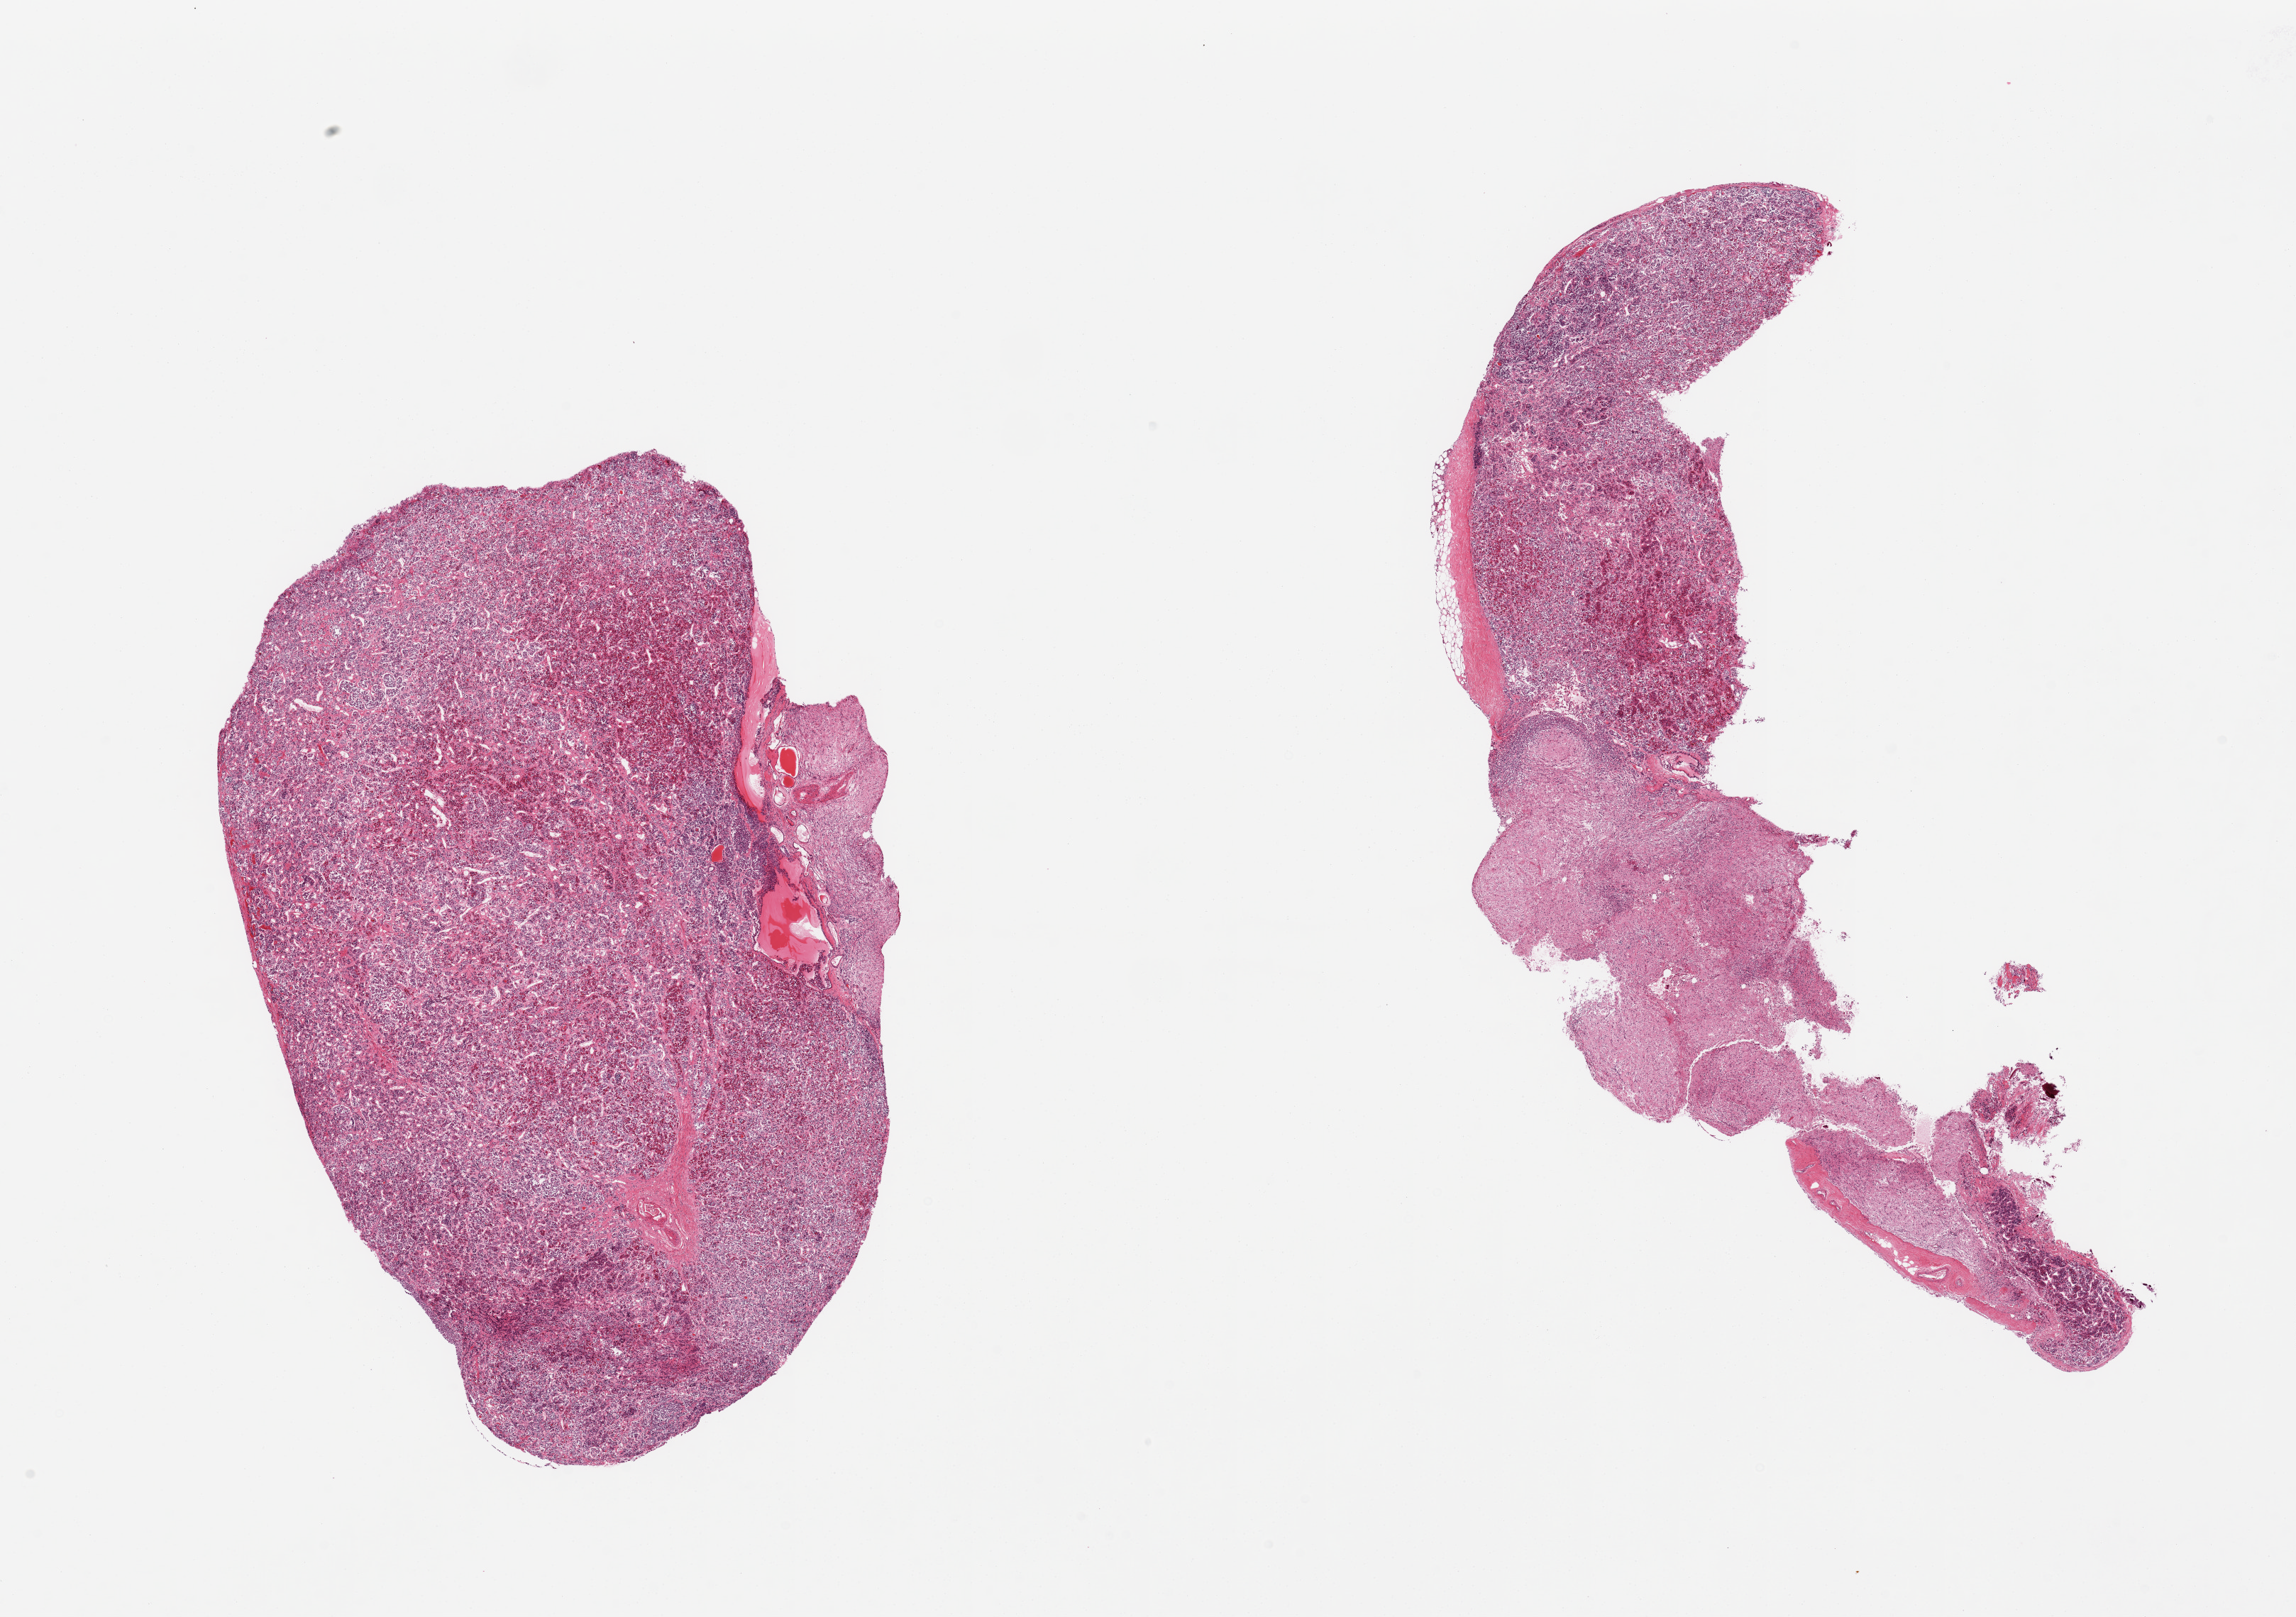
Whole-slide image, hematoxylin and eosin (H&E) stain — shown as a low-resolution overview of the whole scanned area (about 25.6 x 18.0 mm), PAXgene-fixed paraffin-embedded (PFPE) section, sampled site (target tissue): pituitary, donor tissue sample. Donor: male.
* review note (as recorded): 2 pieces, includes adenohypophysis, neurohypopohysis, and pars intermedia